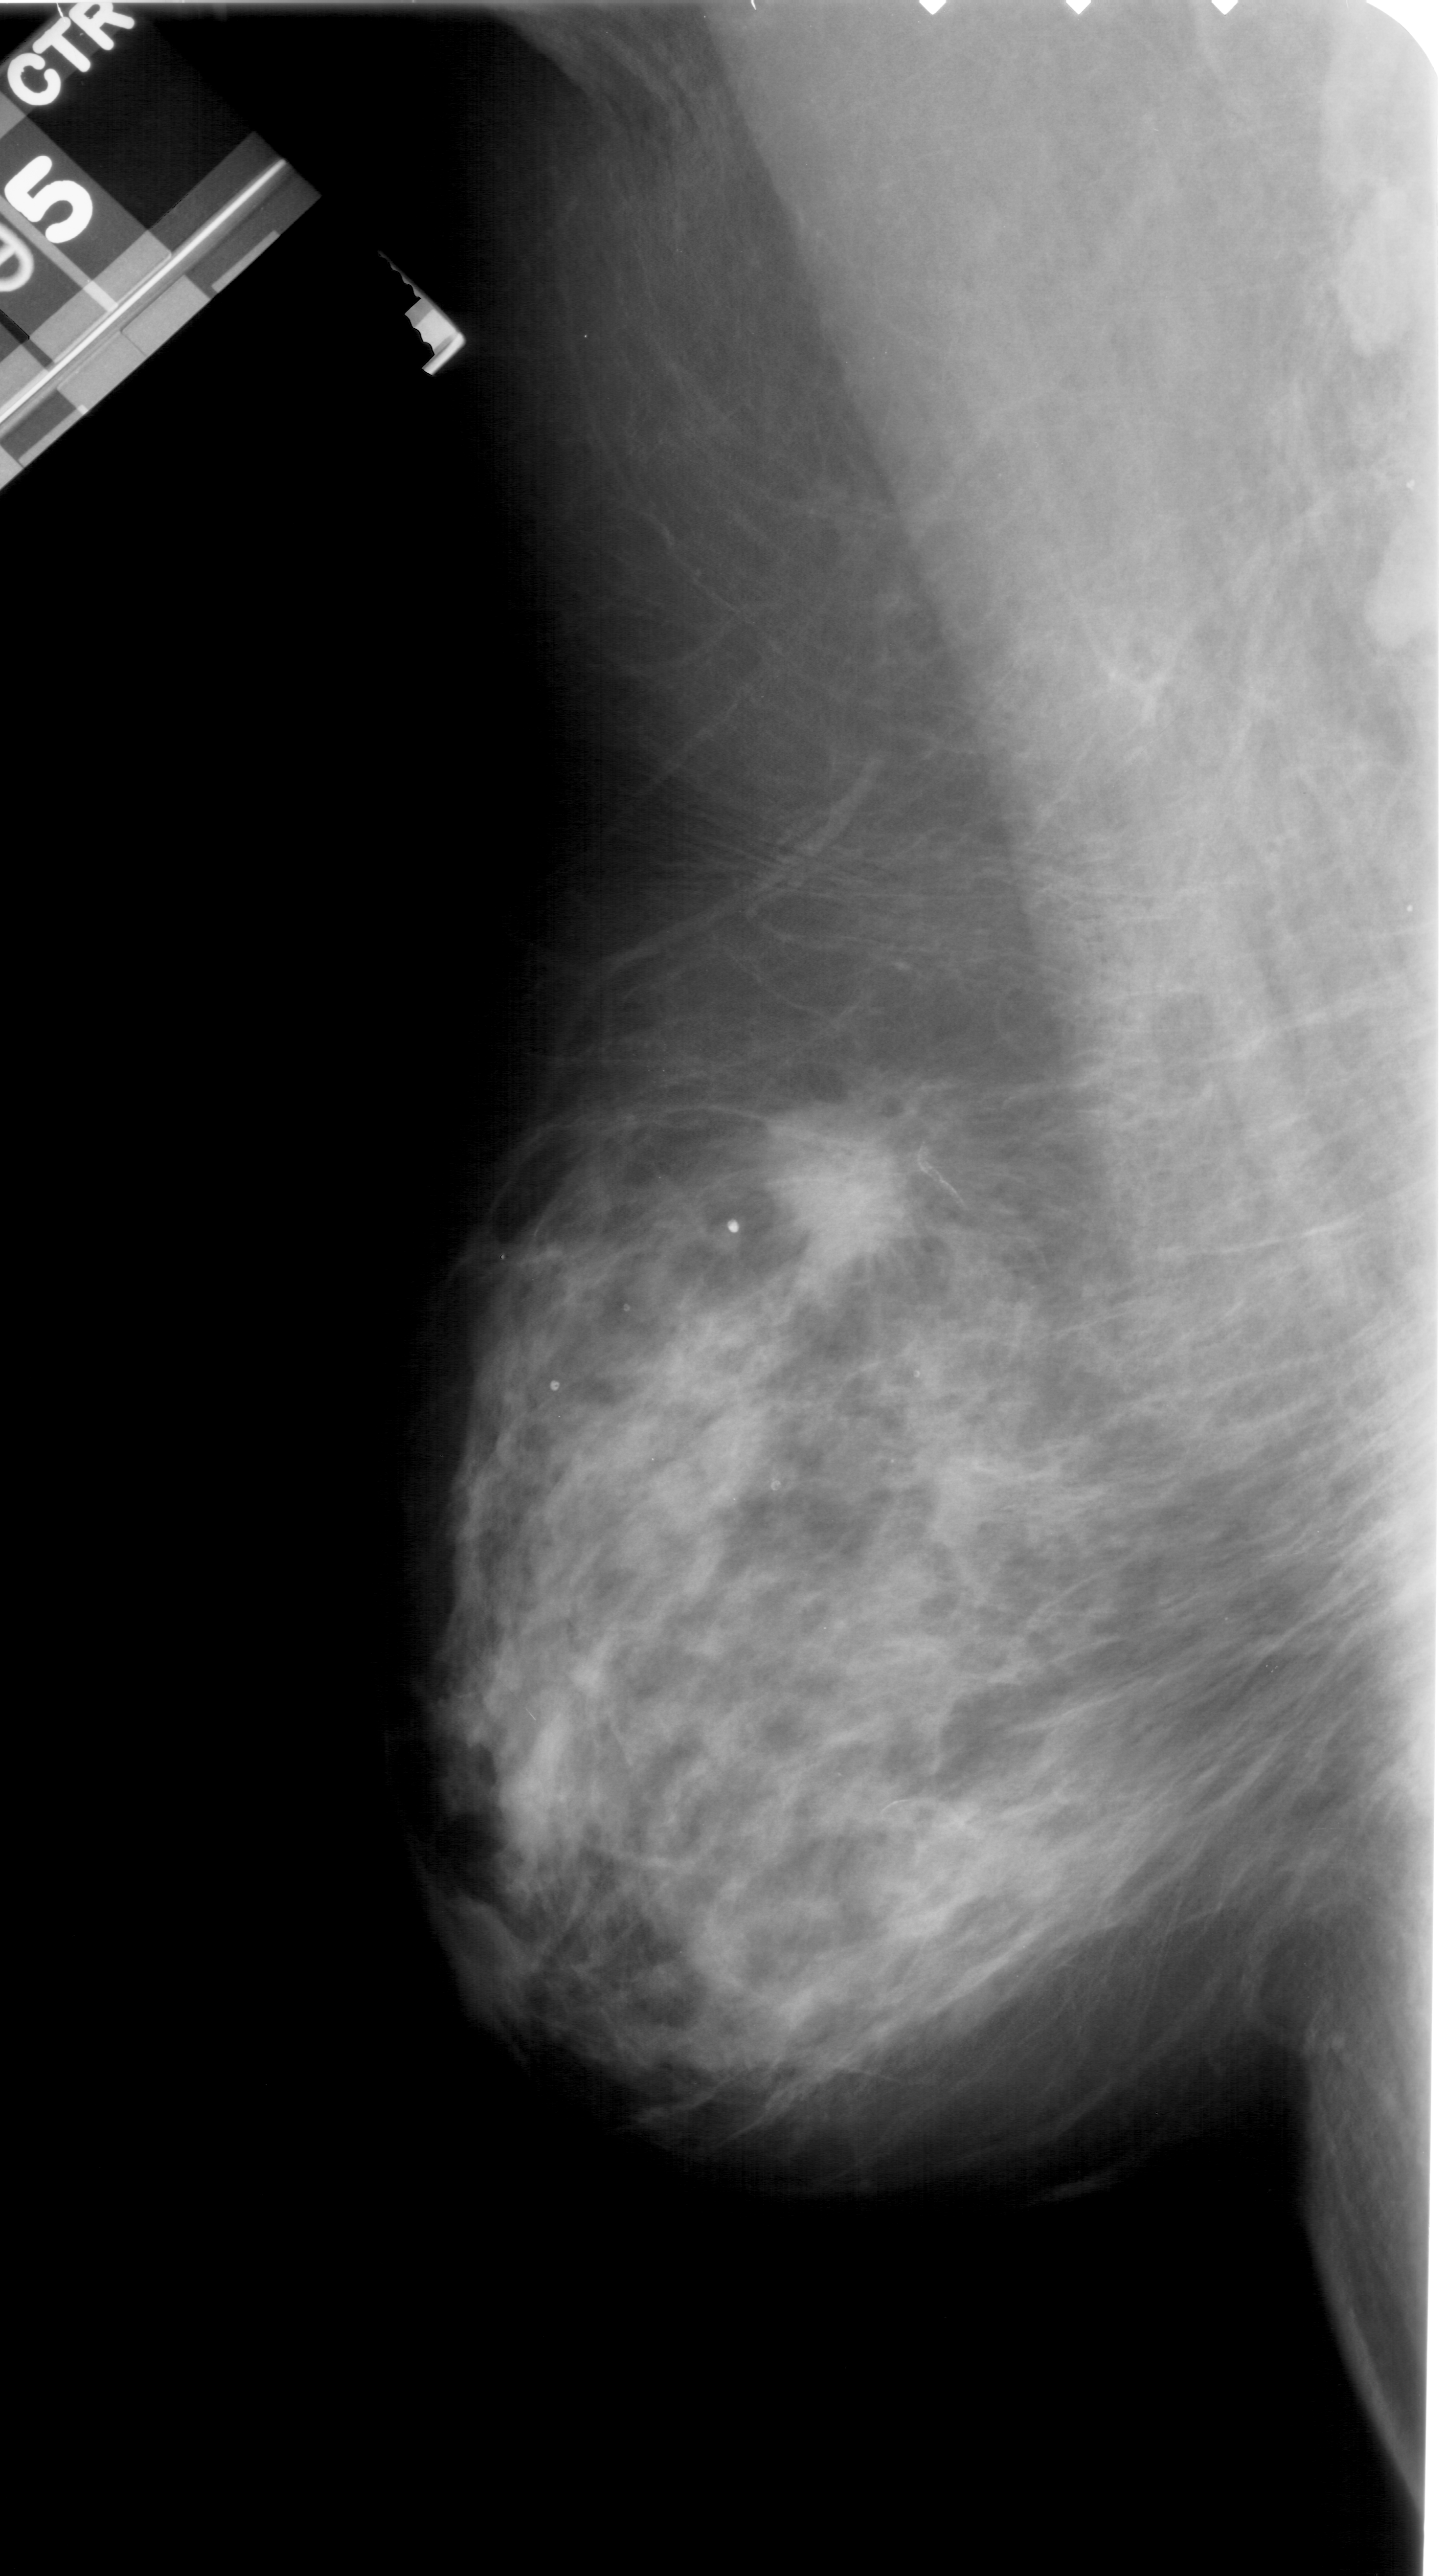
Mammogram (digitized film), left breast, mediolateral oblique (MLO) view, BI-RADS breast density category 3 (scale 1–4).
Marked abnormality: mass, shape irregular, margins spiculated; BI-RADS assessment category 5; pathology (as recorded): malignant.